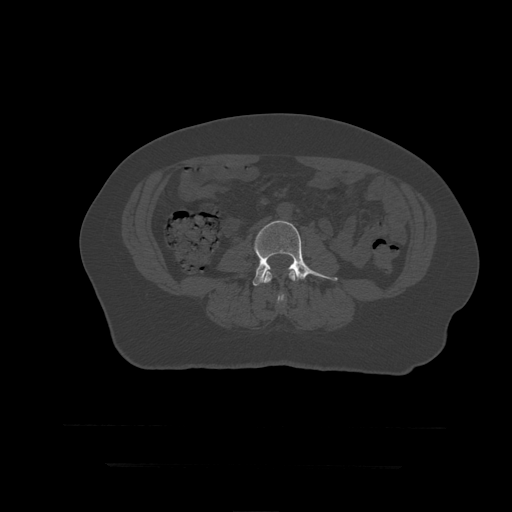
CT including the spine, one axial slice. Position 105 of 399 along the scan axis. Reconstruction kernel STANDARD. 120 kVp. Bone window (W 1800 / L 400 HU). 1.25 mm slice thickness. 512 × 512 image matrix, field of view 450 × 450 mm. Patient age 41 years. Case-level facts recorded for this patient, not image findings: primary cancer: breast.
Annotated regions visible in this slice (semi-automatically segmented with operator editing):
- L3 vertebra: box from (x=263, y=269) to (x=296, y=304) px
- L4 vertebra: (x=253, y=221)–(x=338, y=303)